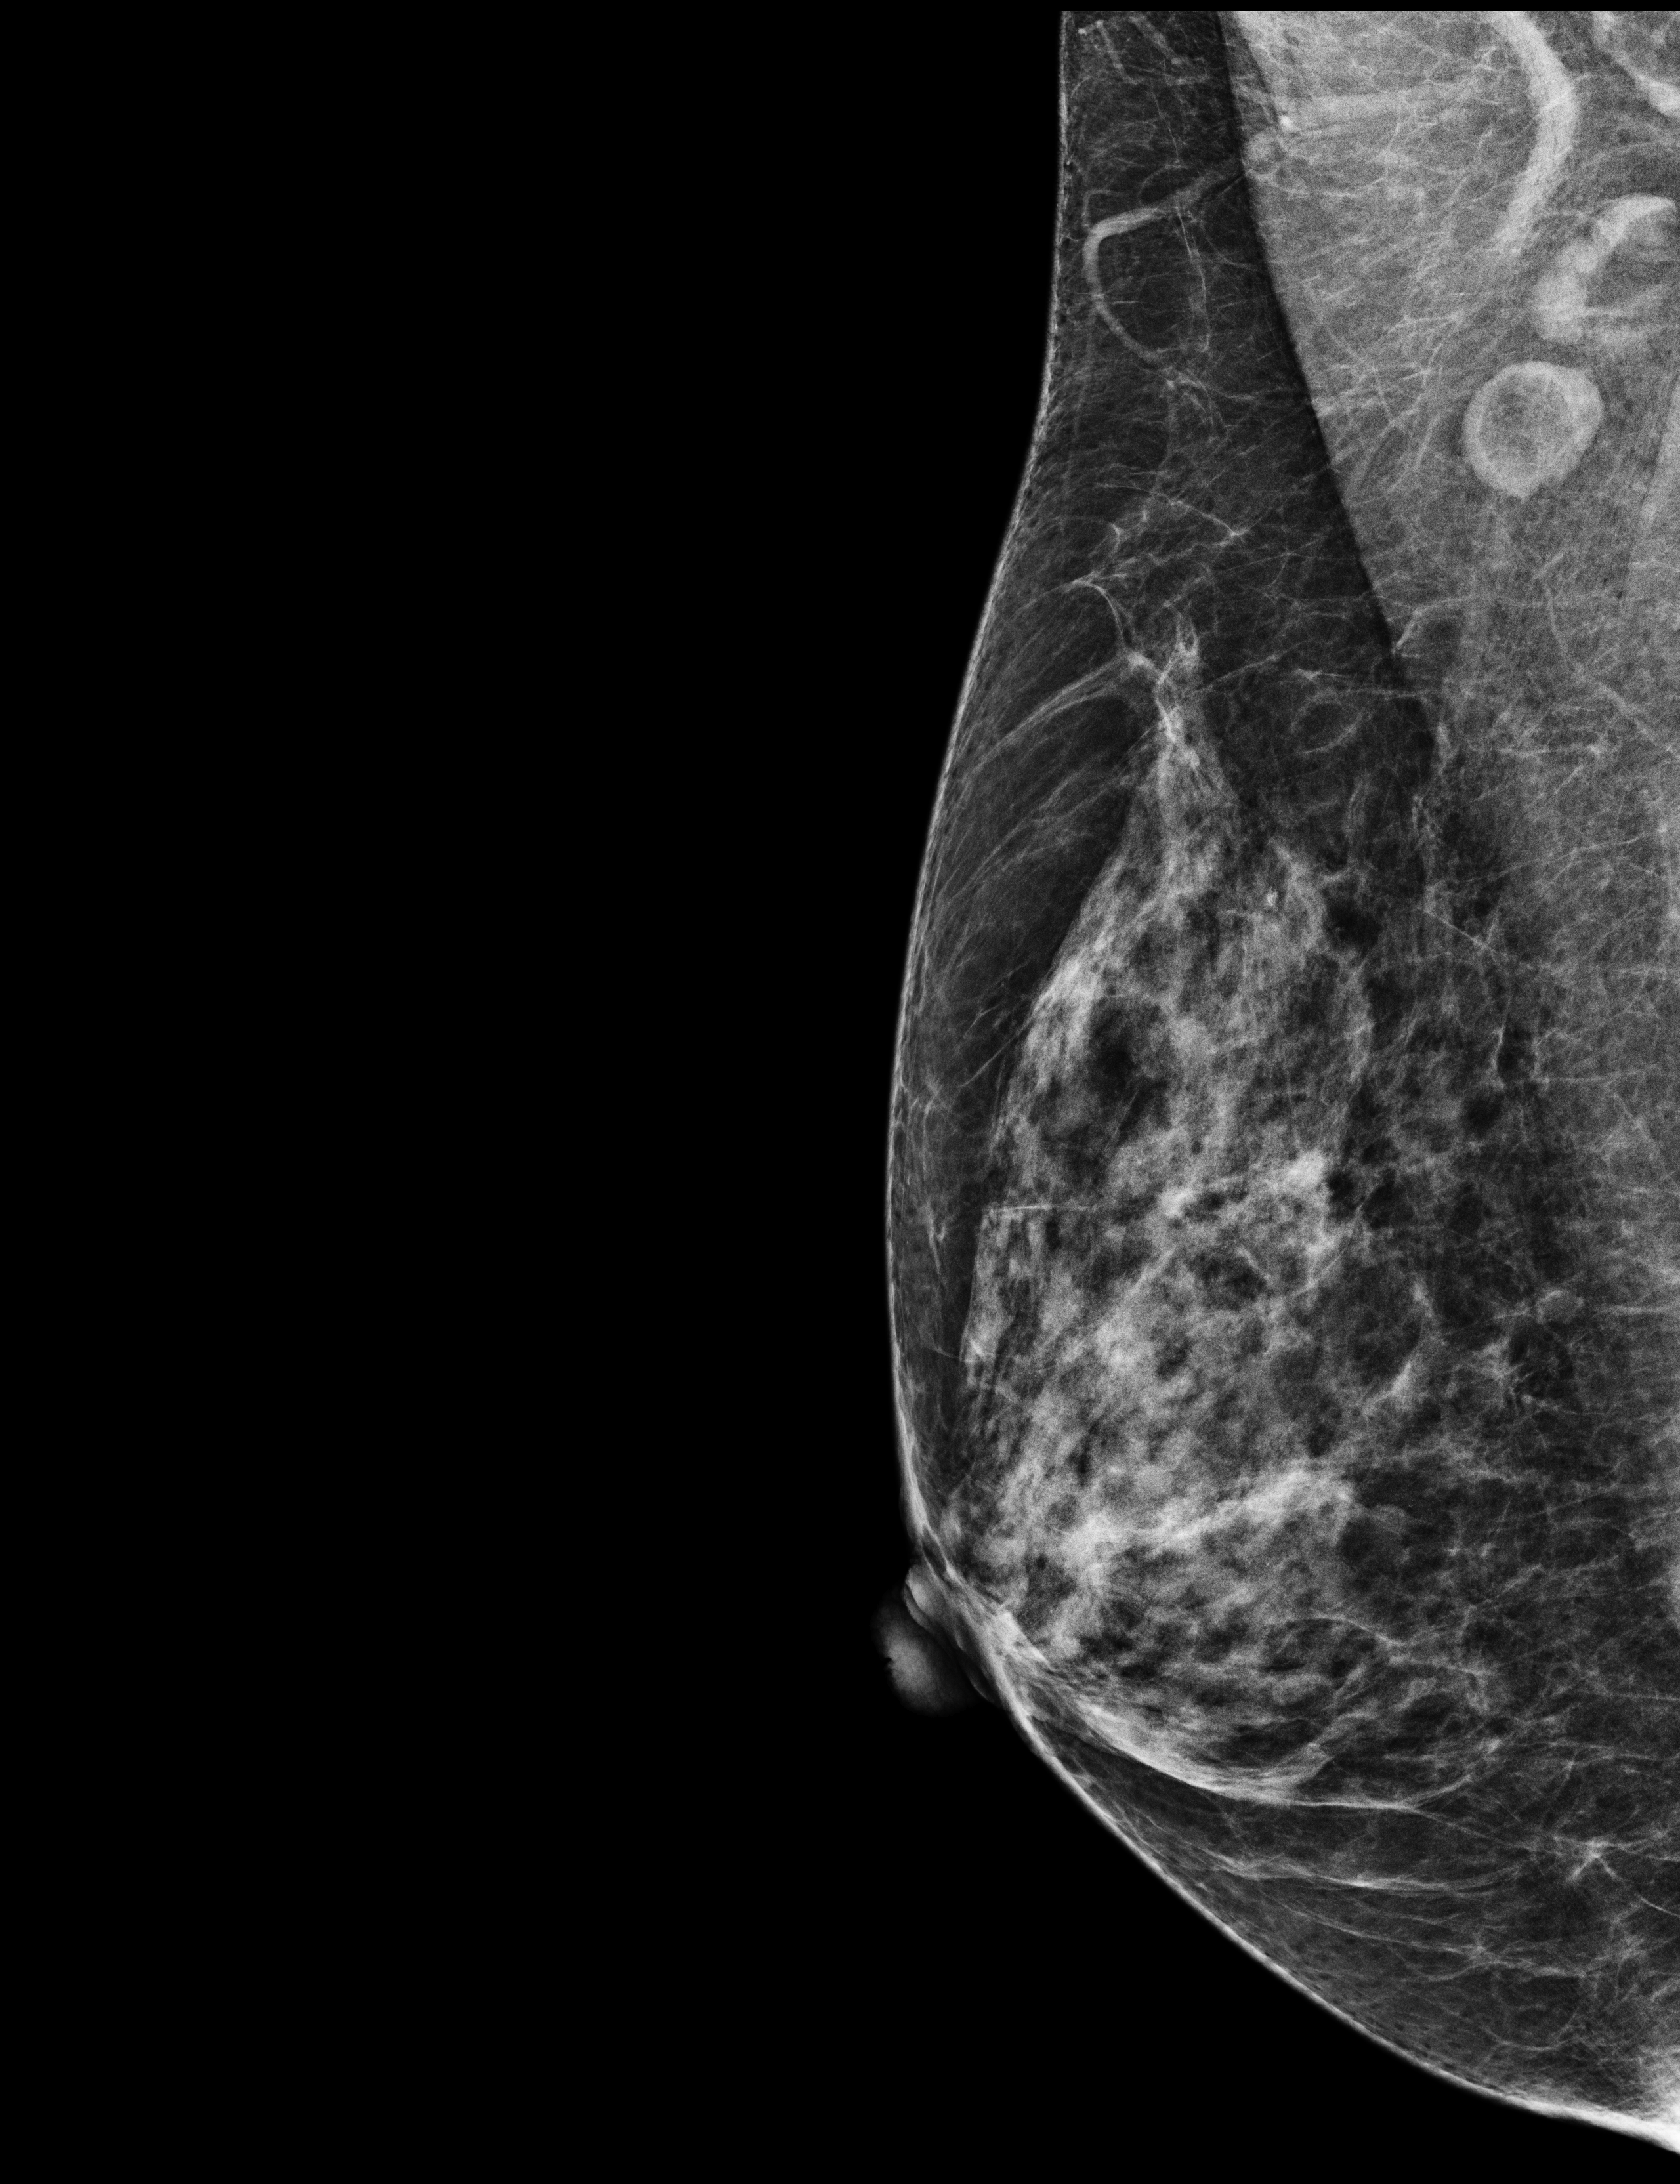
Digital mammogram (FFDM); right breast; mediolateral oblique (MLO) view; screening examination. Female patient, age 60 years.
Breast density at the screening exam (both breasts): heterogeneously dense (BI-RADS density category c). Final BI-RADS assessment for this screening round (tomosynthesis exam, both breasts): category 1. Recall: recalled for additional imaging after this screen.